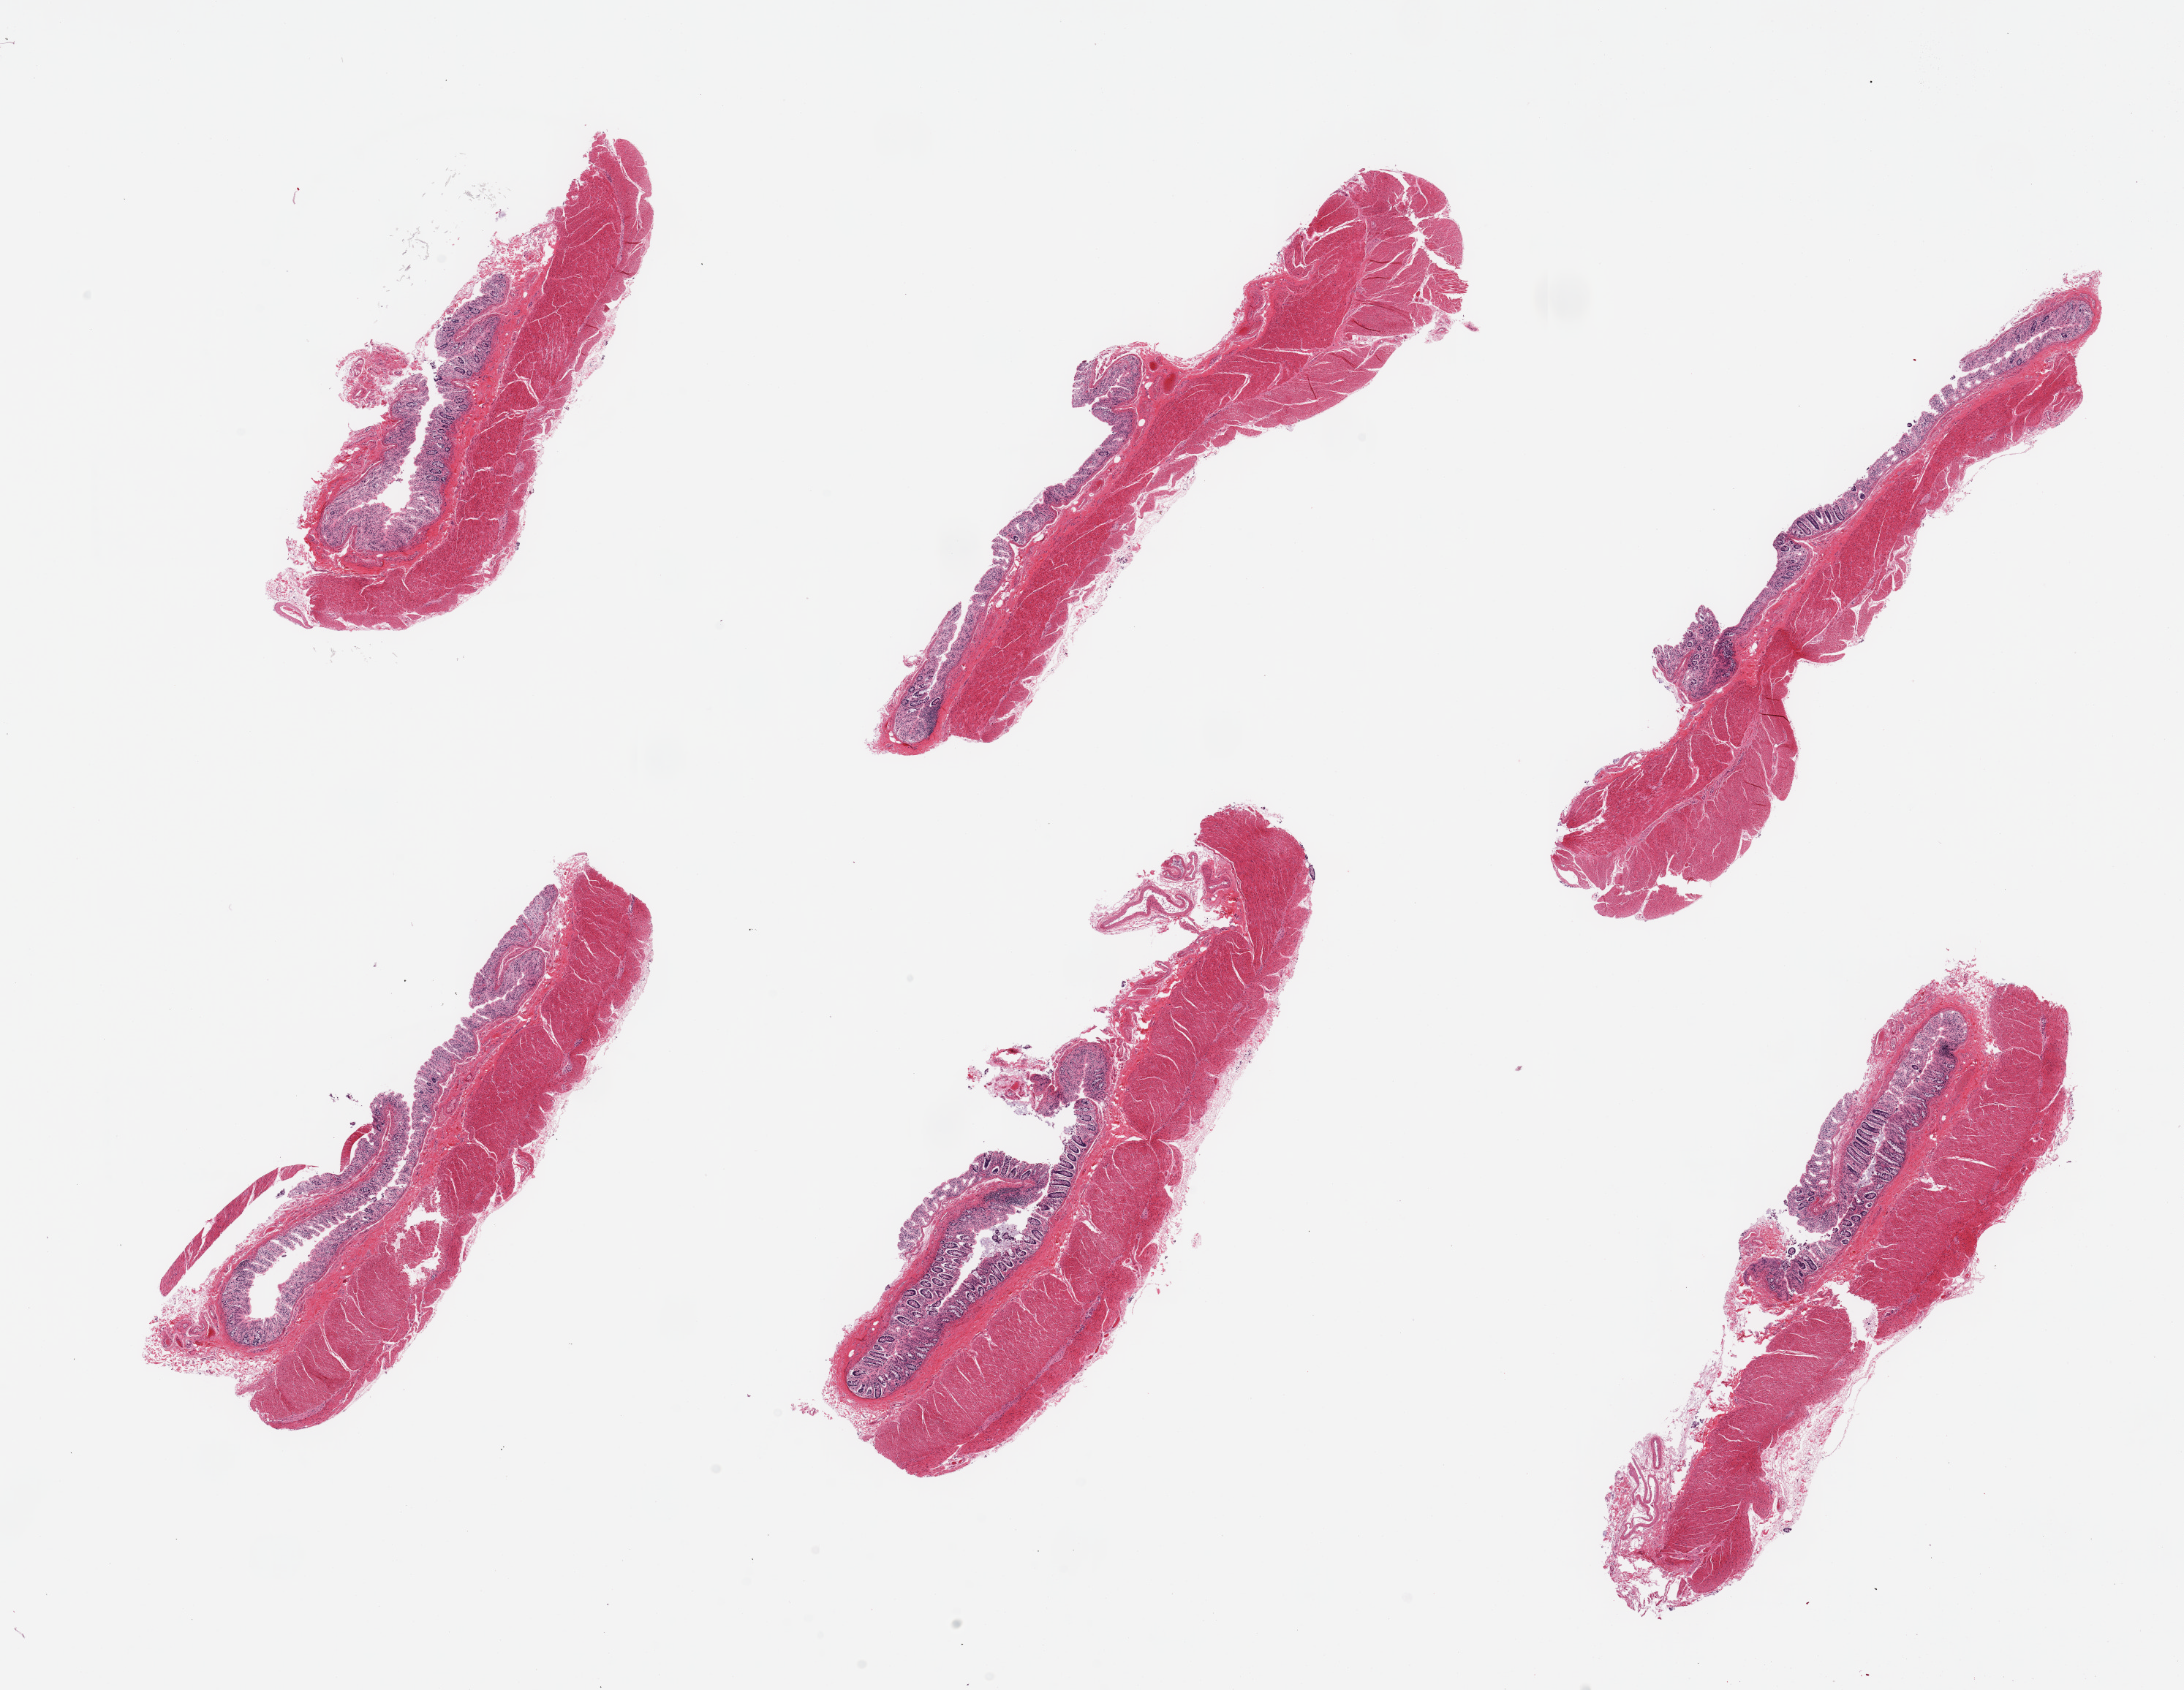
Whole-slide image, hematoxylin and eosin (H&E) stain, brightfield — shown as a low-resolution overview of the whole scanned area (about 23.6 x 18.3 mm, acquisition: 20x scan); PAXgene-fixed paraffin-embedded (PFPE) section; section of transverse colon (target tissue); donor tissue sample. Donor: male.
Reviewer comment on this tissue sample: 6 pieces; extensive glandular autolysis except for foci of moderate autolysis; muscle intact.